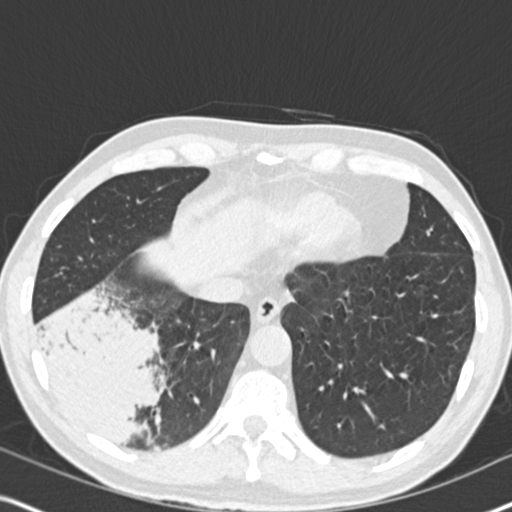
Chest CT (low-dose screening protocol), one axial image, second annual screen, lung window (W 1500 / L -600 HU), 2 mm slice thickness, slice 123 of 182 in the series. Male, age 61 years at enrolment.
• Expert reader's lesion annotation, bounding box <30,296,183,458> (left, top, right, bottom; pixels).
• Reader record for this screening exam (exam-level; its link to the box is not recorded): non-calcified nodule or mass ≥4 mm, right lower lobe, 90 × 80 mm, soft tissue attenuation, pre-existing on the prior screen: yes; interval growth: yes.
• Lung cancer was diagnosed 20 days after this screen: bronchiolo-alveolar adenocarcinoma, NOS, right lower lobe, moderately differentiated (G2), stage IIIB (AJCC 6th edition), 90 mm at pathology.